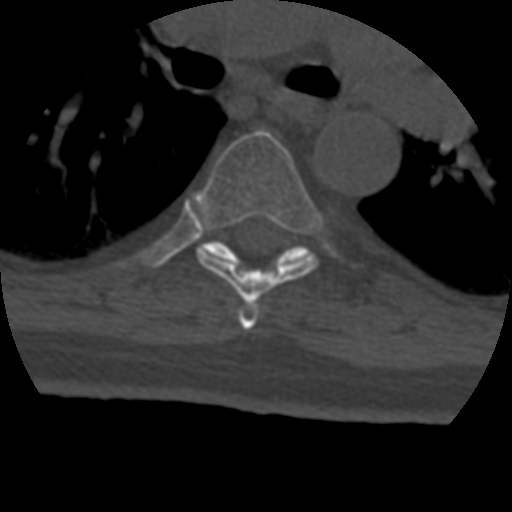
CT including the spine, one axial slice; position 296 of 399 along the scan axis; reconstruction kernel STANDARD; 120 kVp; bone window (W 1800 / L 400 HU); 1.25 mm slice thickness; 512 × 512 image matrix. Patient age 69 years. Case-level facts recorded for this patient, not image findings: primary cancer: prostate.
Structures marked on this image (semi-automatically segmented with operator editing):
- T5 vertebra: bounding box [x1, y1, x2, y2] px = [239, 304, 259, 330]
- T6 vertebra: [196, 131, 322, 304]
- T7 vertebra: [203, 241, 312, 265]